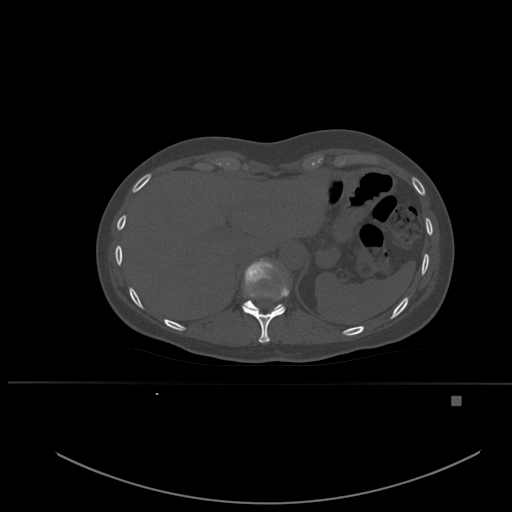
CT including the spine, one axial slice. Slice 283 of 651 in the series (ordered by position). Bone window (W 1800 / L 400 HU). 1.5 mm slice thickness. 512 × 512 image matrix. Patient: female, 49 years. From the clinical record (not read from this slice): primary cancer: breast.
Annotated regions visible in this slice (semi-automatically segmented with operator editing):
- T10 vertebra: bounding box <242,276,290,343> (left, top, right, bottom; pixels)
- T11 vertebra: <242,259,283,311>